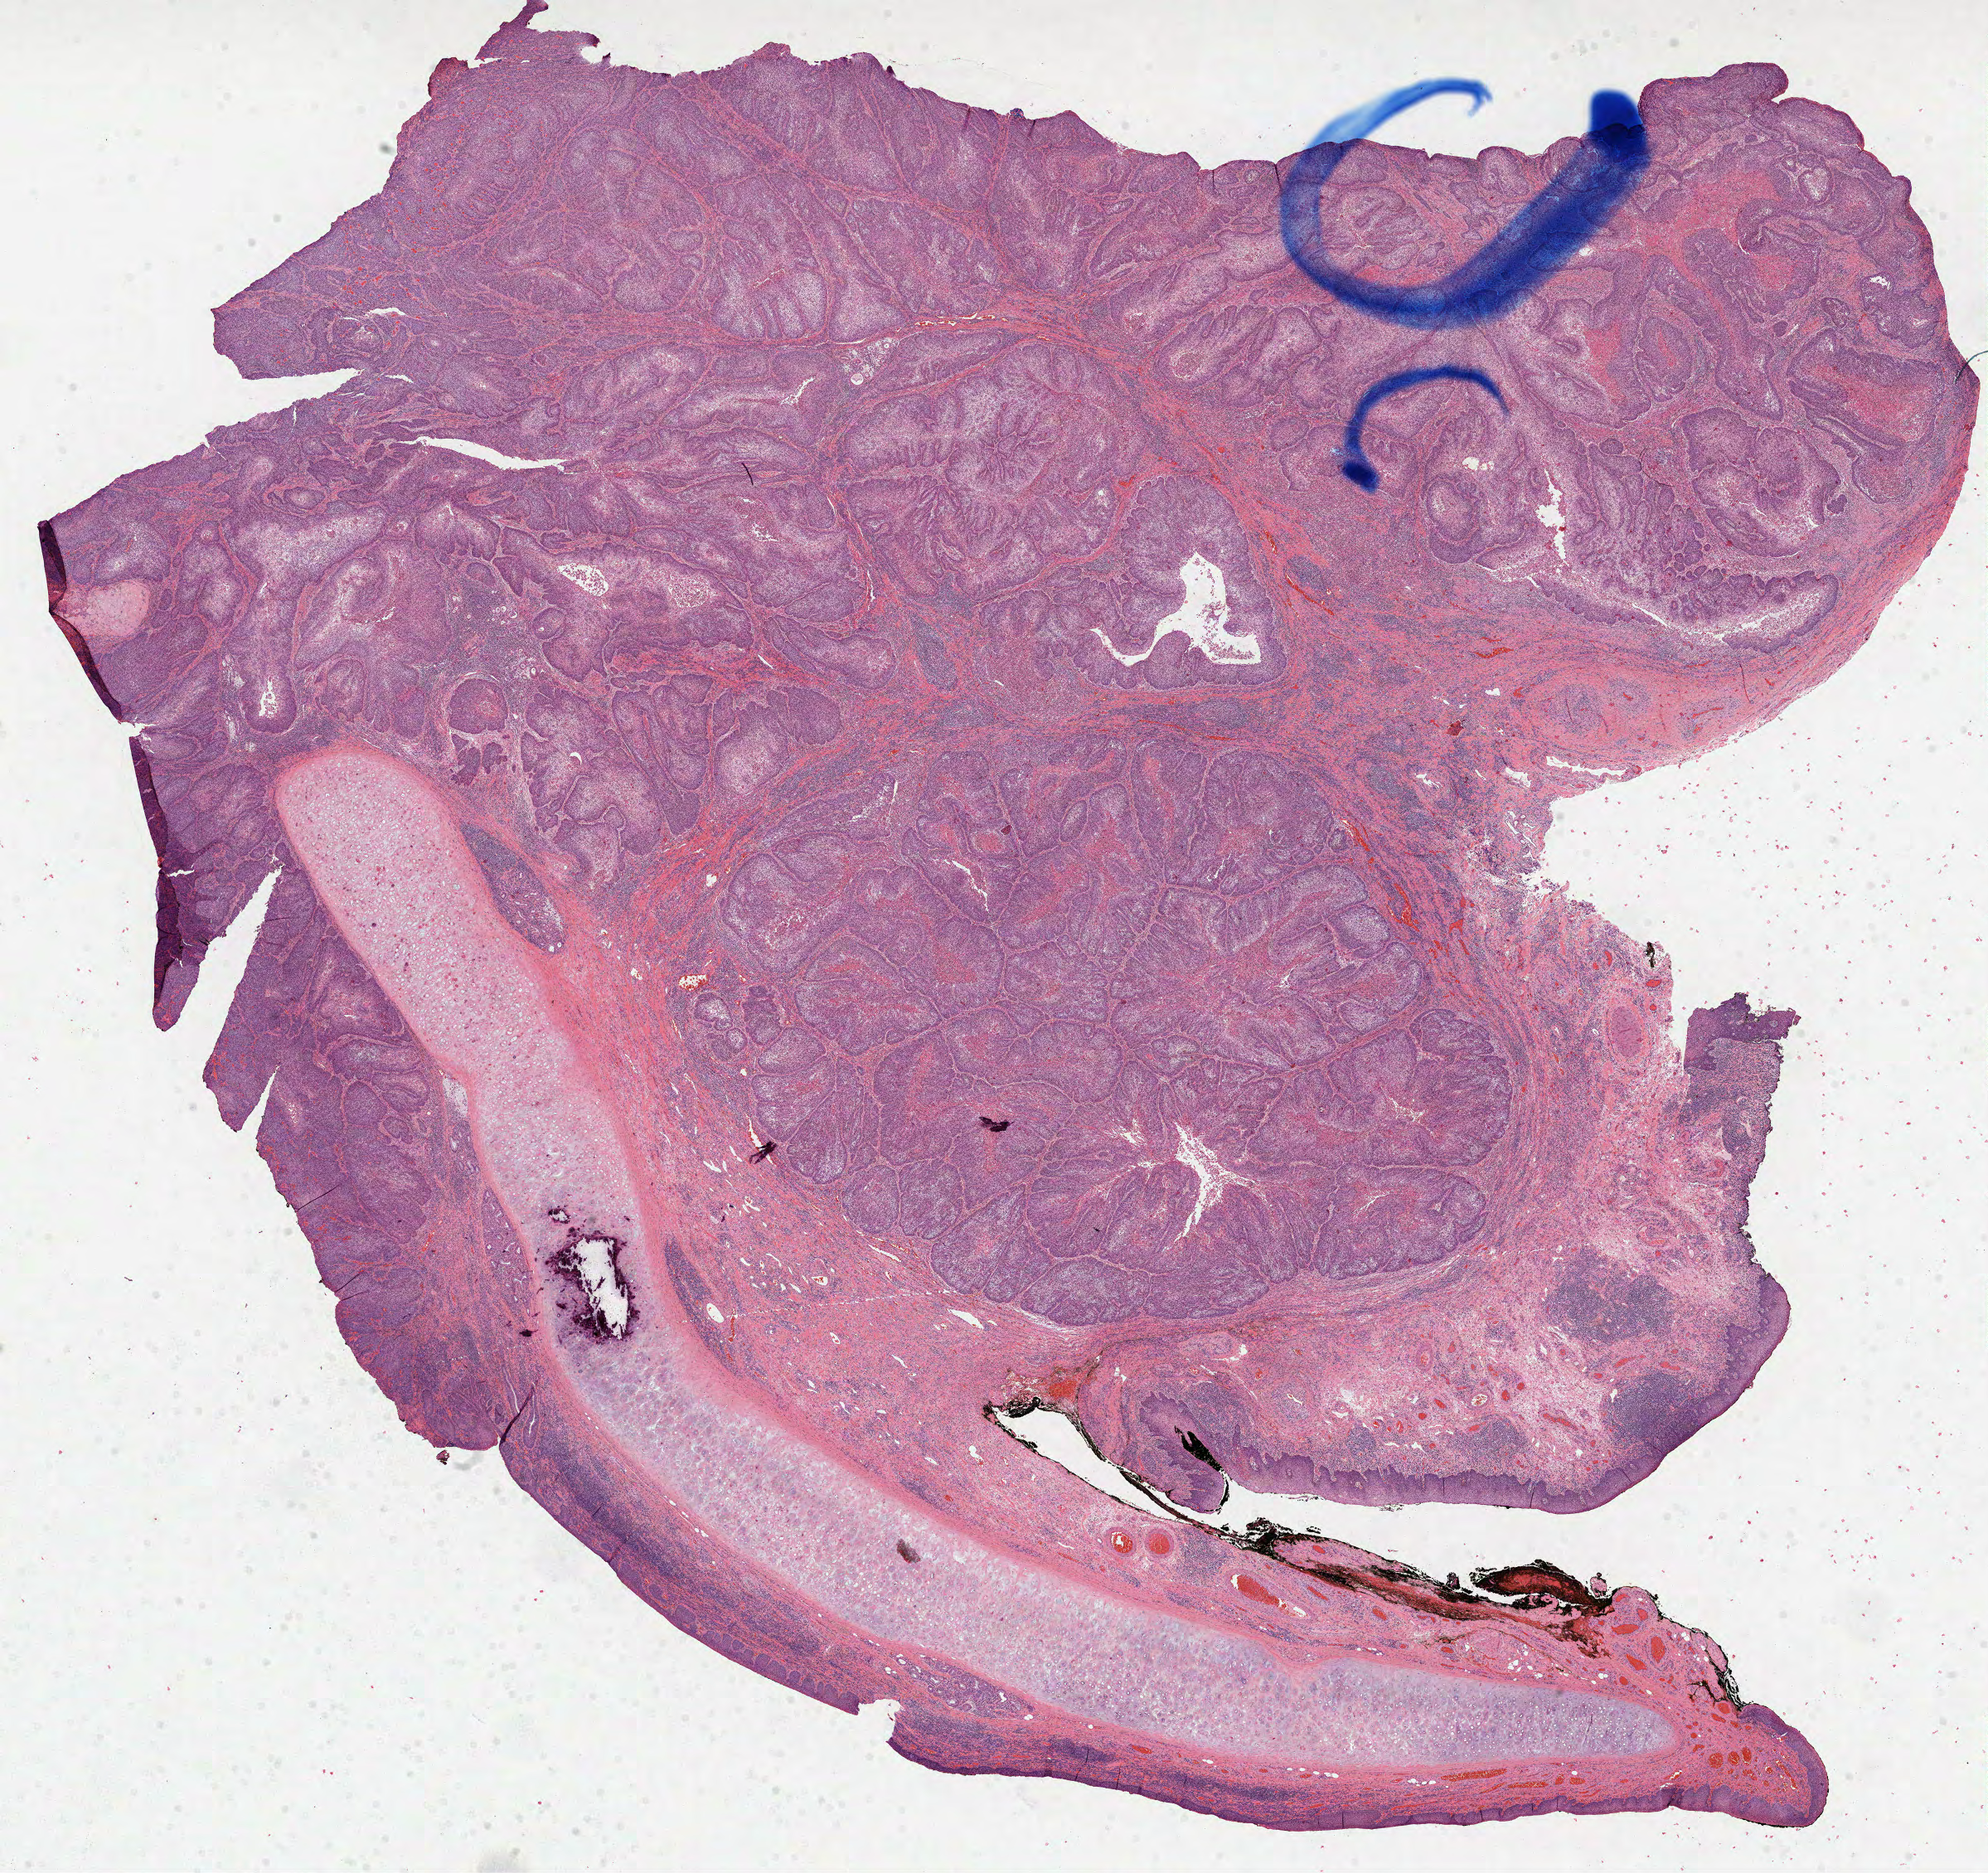
Digitized H&E-stained tissue section (whole slide) — a low-resolution overview of the entire scanned area, about 19.3 x 18.2 mm (acquisition: 40x scan), FFPE section, primary tumour sample from the head and neck. Male, age 62 years at initial diagnosis. Histologic grade: G2 (moderately differentiated).
• AJCC pathologic stage: III (7th edition)
• pathologic diagnosis: Squamous cell carcinoma, NOS (larynx, NOS)
• laterality: left